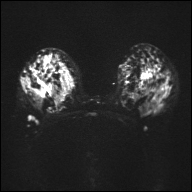
Breast MRI, one axial slice; slice 23 of 32 in the series (ordered by position); diffusion-weighted series; image 2 of 4 stored at this slice position (different b-values; order by instance number); 1.5 T; 4 mm slice thickness; 192 × 192 image matrix, field of view 360 × 360 mm. Female patient.
Annotated regions visible in this slice (manually delineated by an expert):
- tumour on diffusion-weighted imaging: bounding box (x1, y1, x2, y2) in pixels: (36, 72, 62, 105)